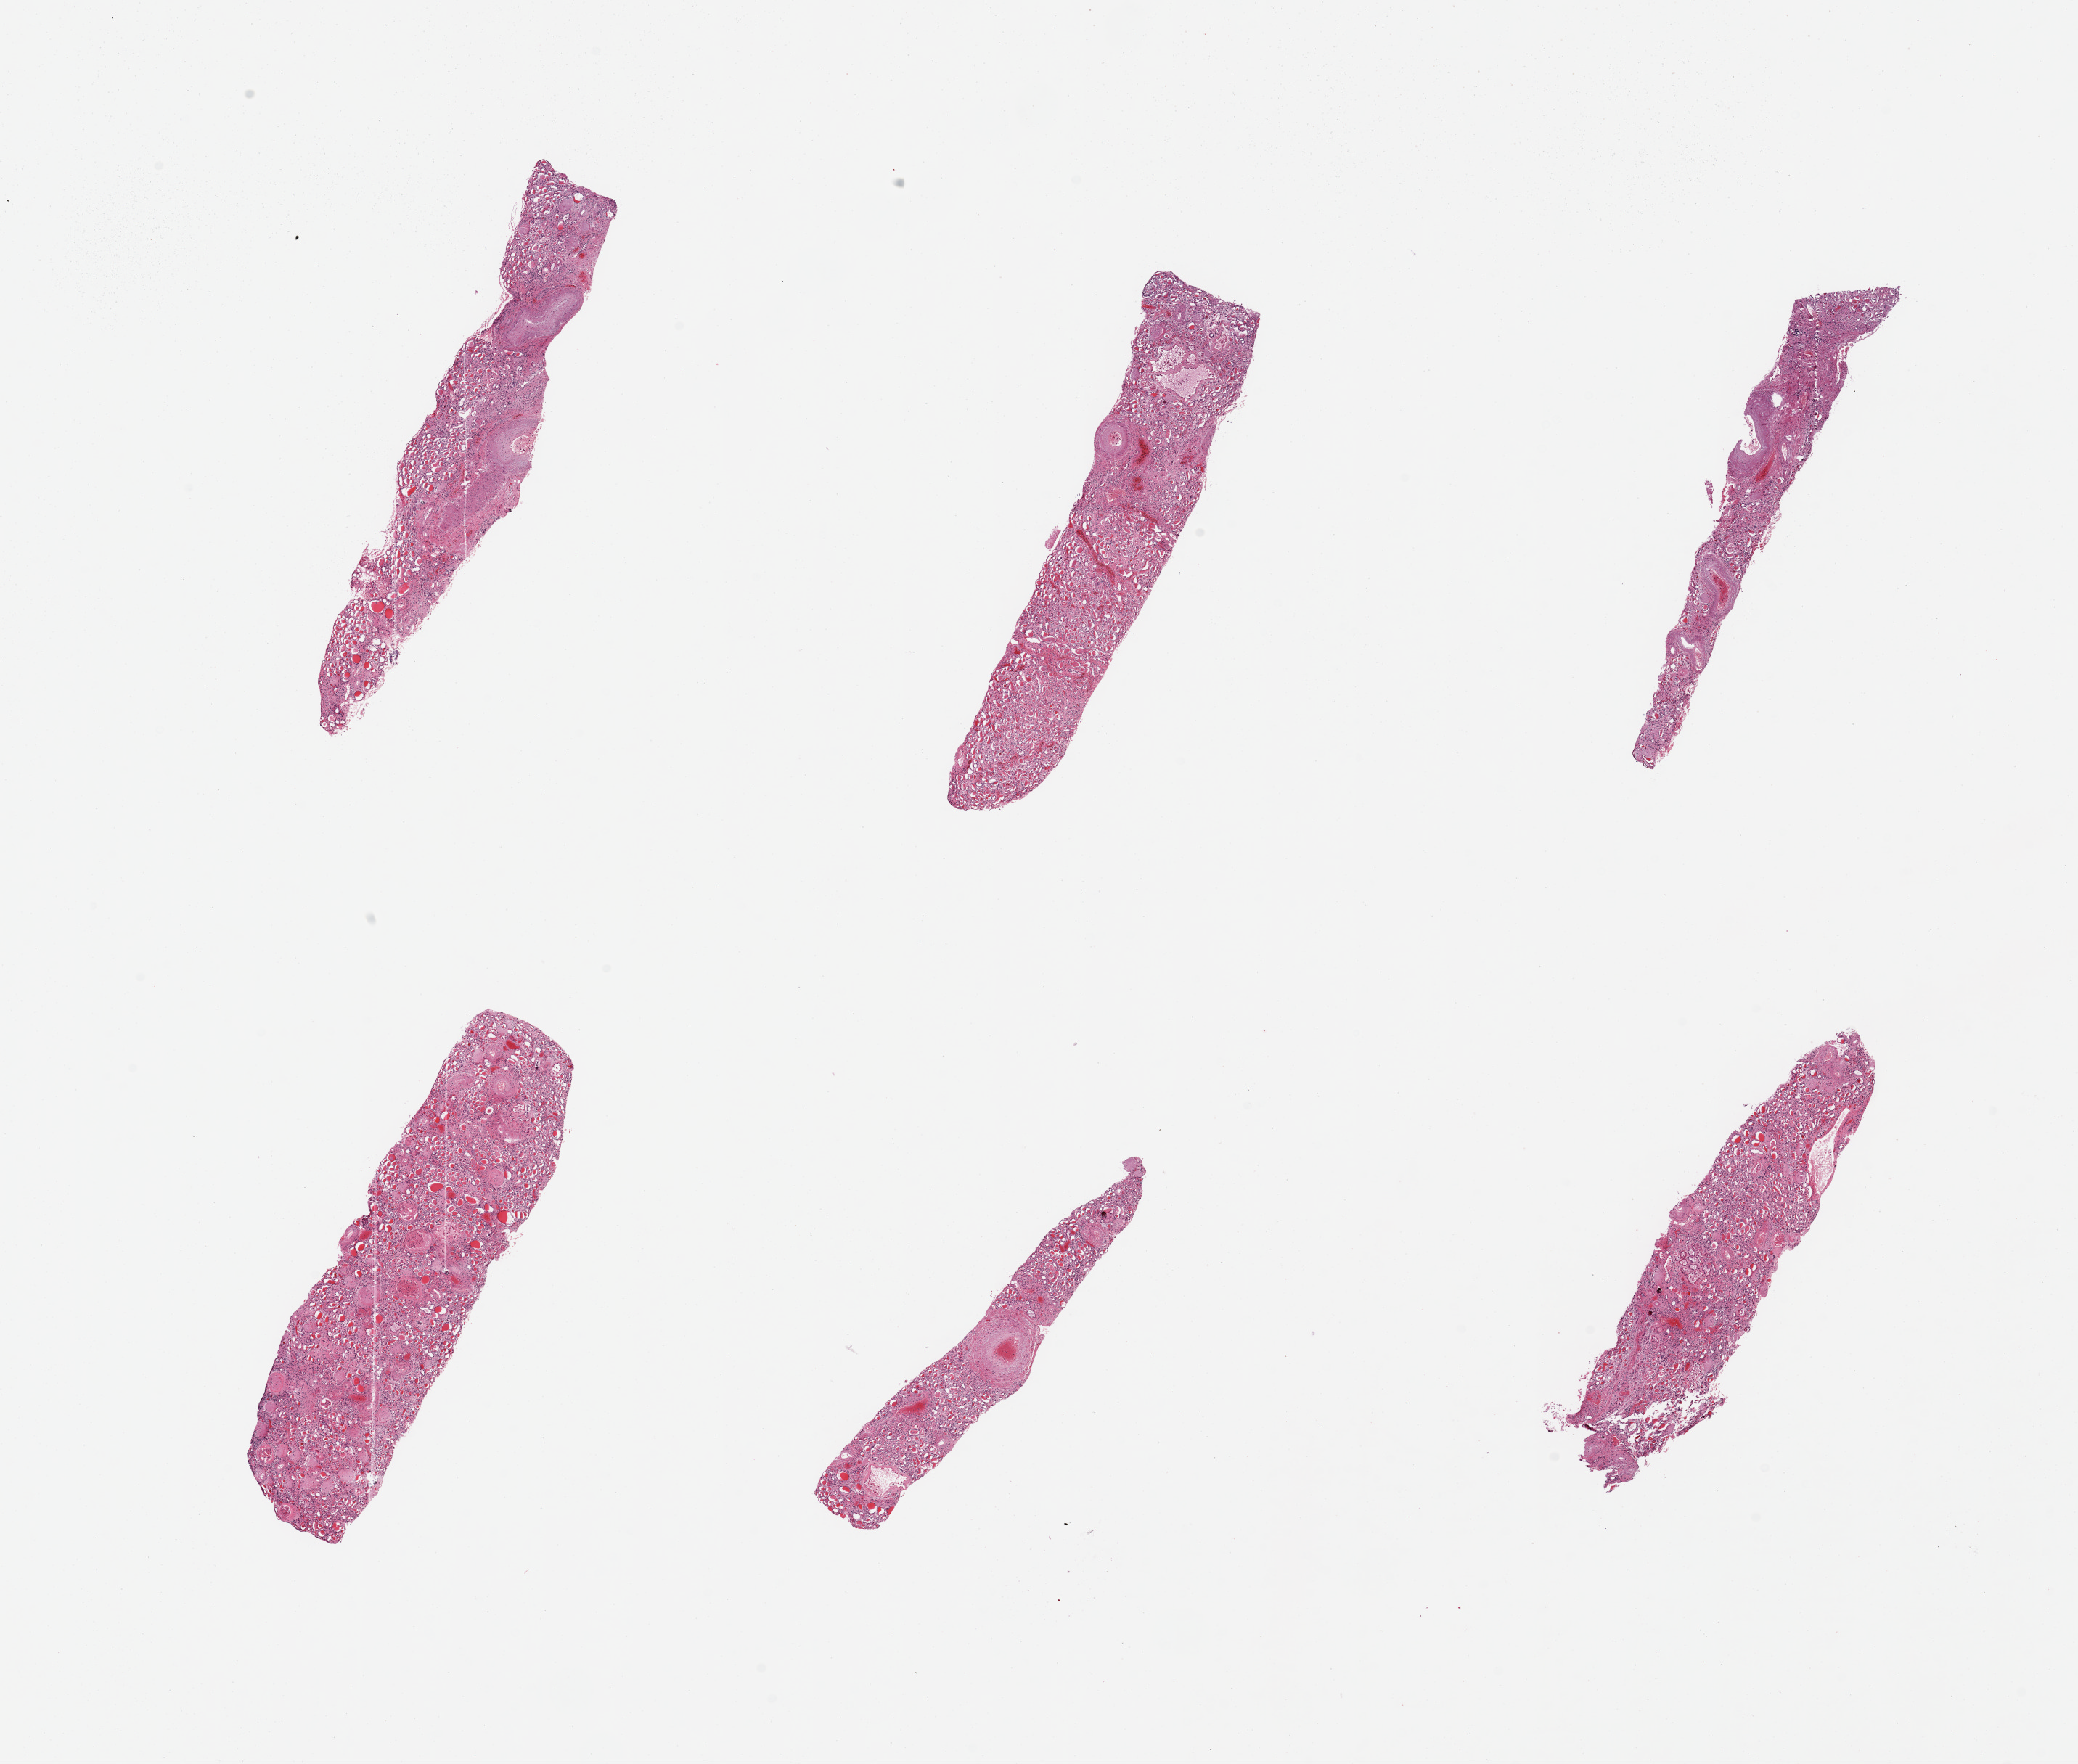
H&E whole-slide image, whole scanned area (about 22.6 x 19.2 mm, acquisition: 20x scan) shown as a low-resolution overview; PAXgene-fixed, paraffin-embedded tissue; sampled site (target tissue): renal cortex; tissue donor sample. Donor: female.
* reviewer comment on this tissue sample: 6 pieces,largely medulla. Marked thyroidization, chronic nepritis